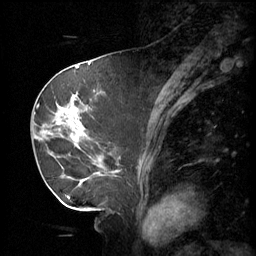
Breast MRI (dynamic contrast-enhanced), one sagittal slice; position 25 of 60 along the scan axis; 3 images stored at this slice position (order not interpretable as contrast timing); 1.5 T; TE 4.2 ms, TR 11 ms; 256 × 256 image matrix, field of view 220 × 220 mm. Female patient, age 69 years.
Annotated regions visible in this slice (semi-automatically segmented with operator editing):
- analysis volume of interest (the breast-tissue region the enhancement analysis was run in; not a lesion): bounding box <36,88,116,189> (left, top, right, bottom; pixels)
- tumour enhancement mask (voxels above the 70 % enhancement threshold inside the analysis volume of interest): <57,96,103,175>